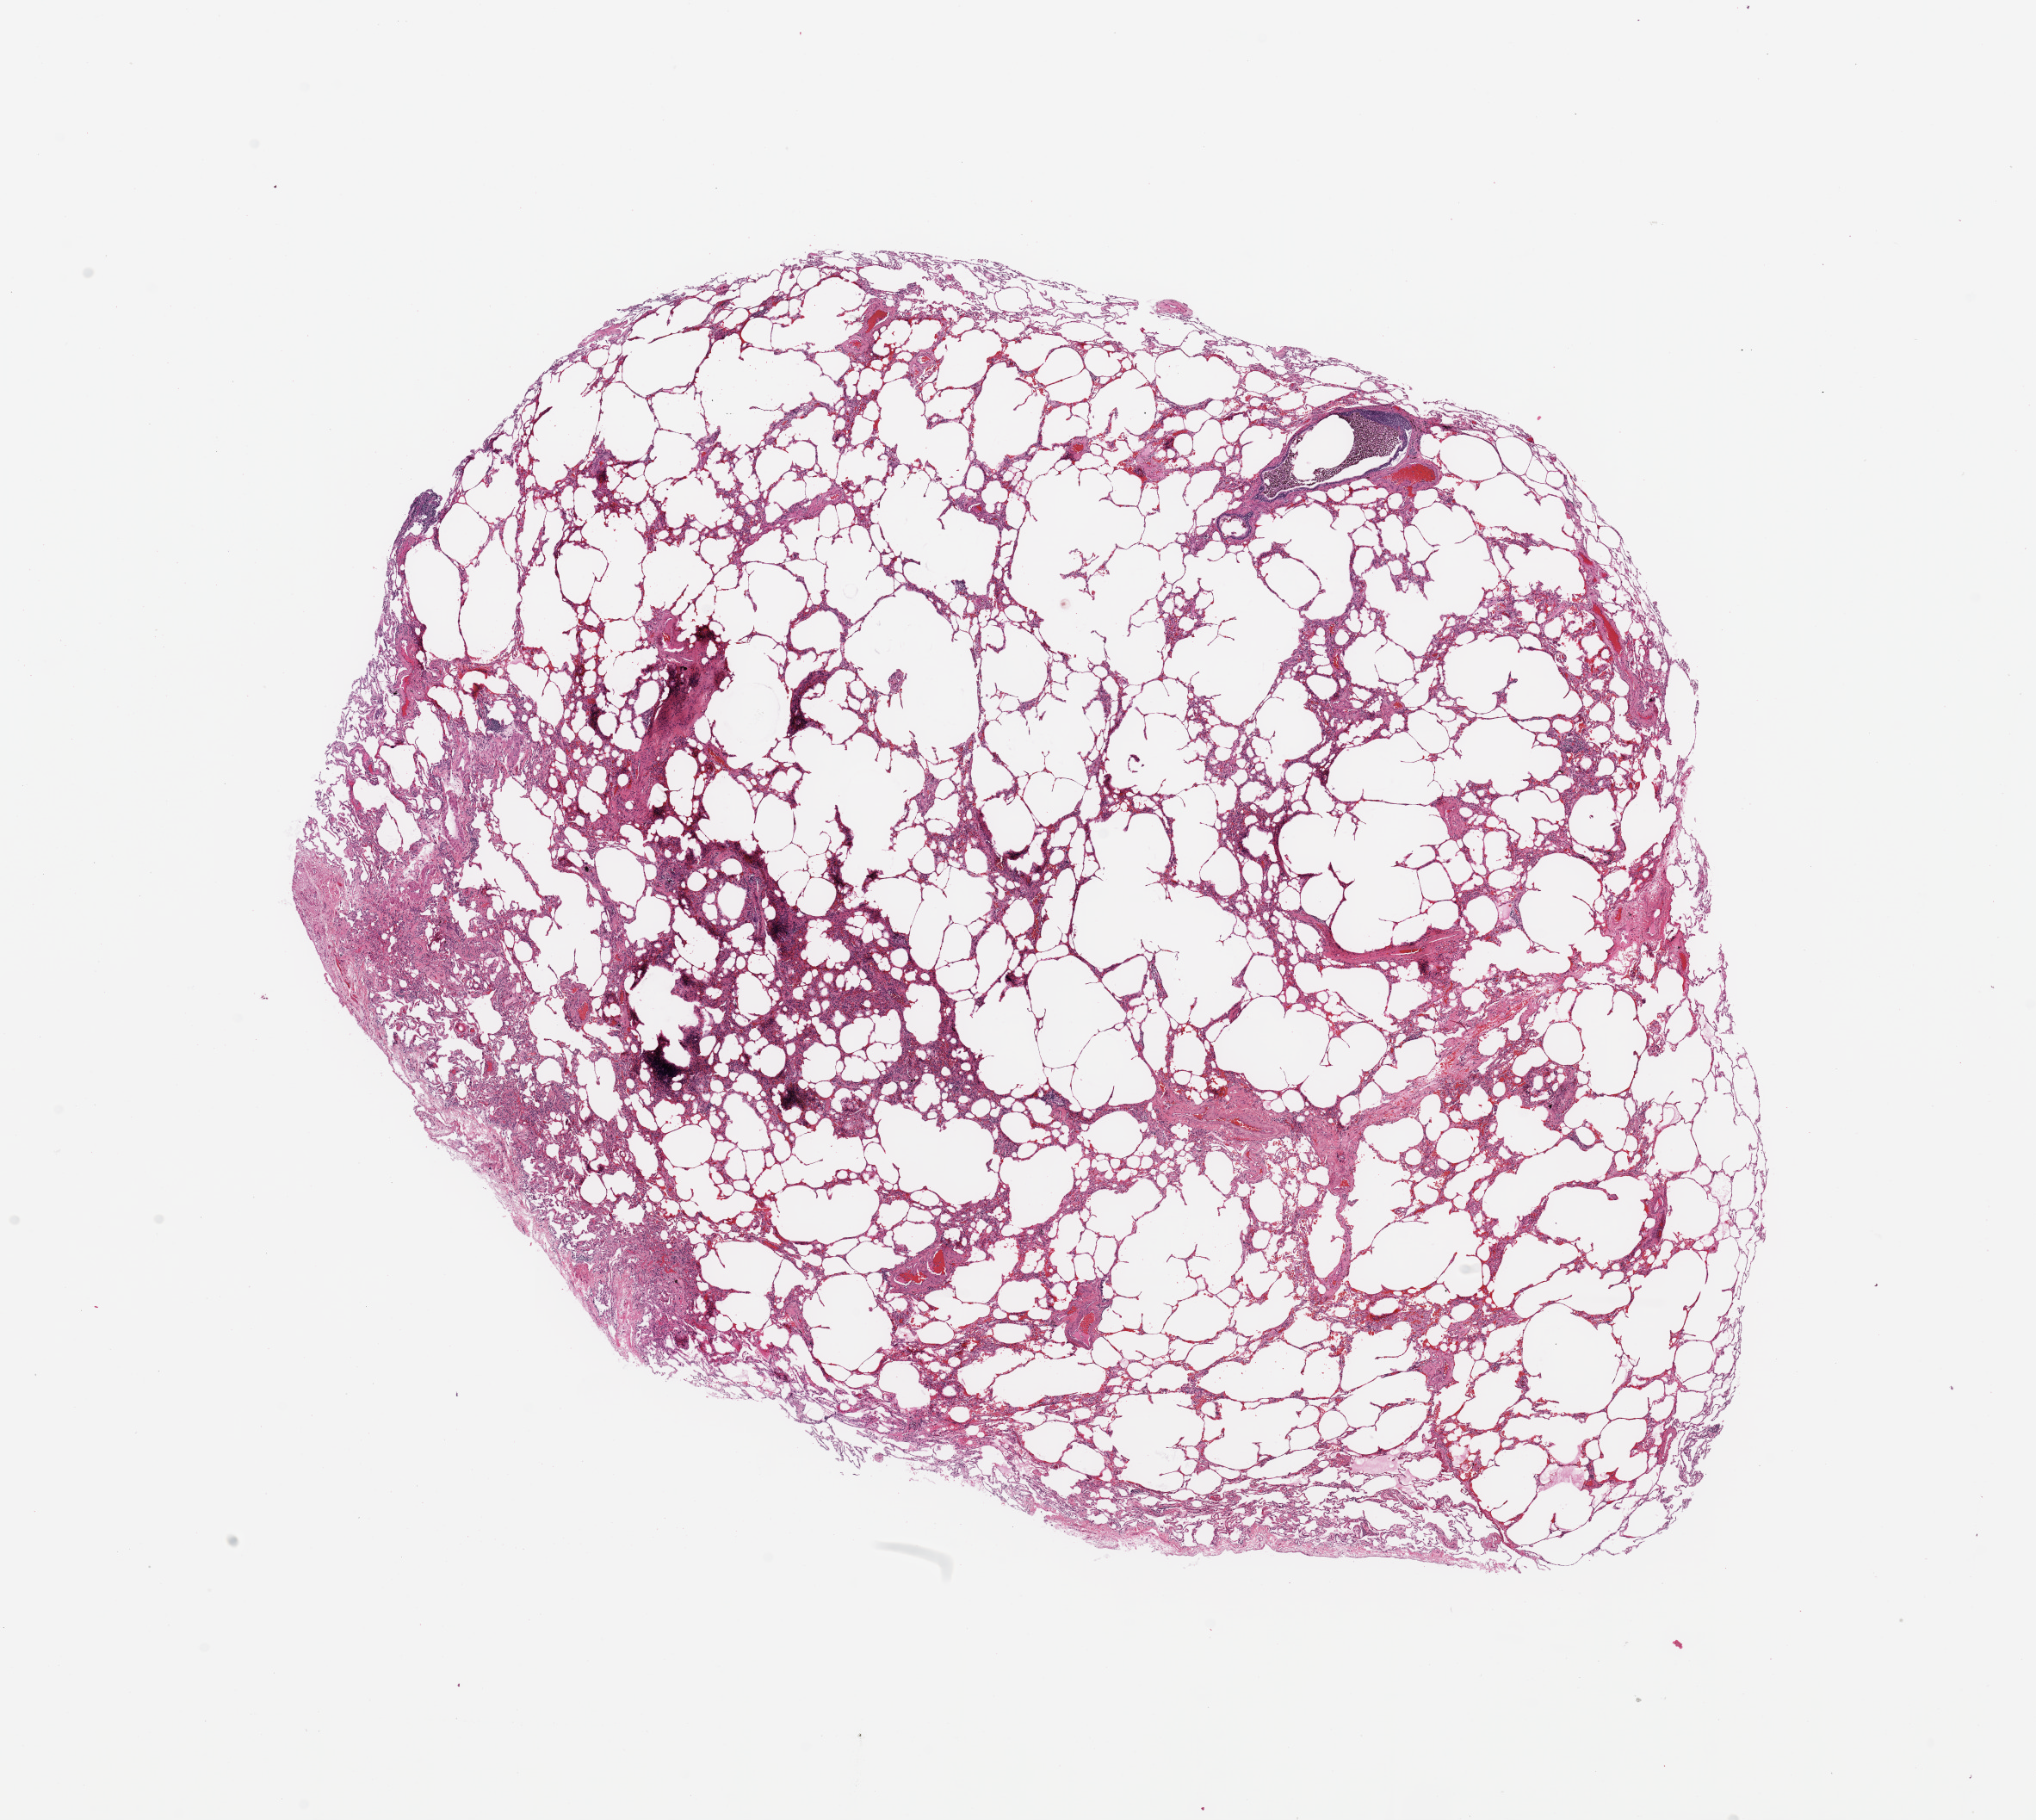
Digitized H&E tissue section (whole slide), whole scanned area (about 18.7 x 16.7 mm) shown as a low-resolution overview. Lung, normal (non-tumour) tissue. Patient: male, age 76 years.
• this section: normal (non-tumour) tissue from the same patient
• patient diagnosis: Adenocarcinoma, NOS